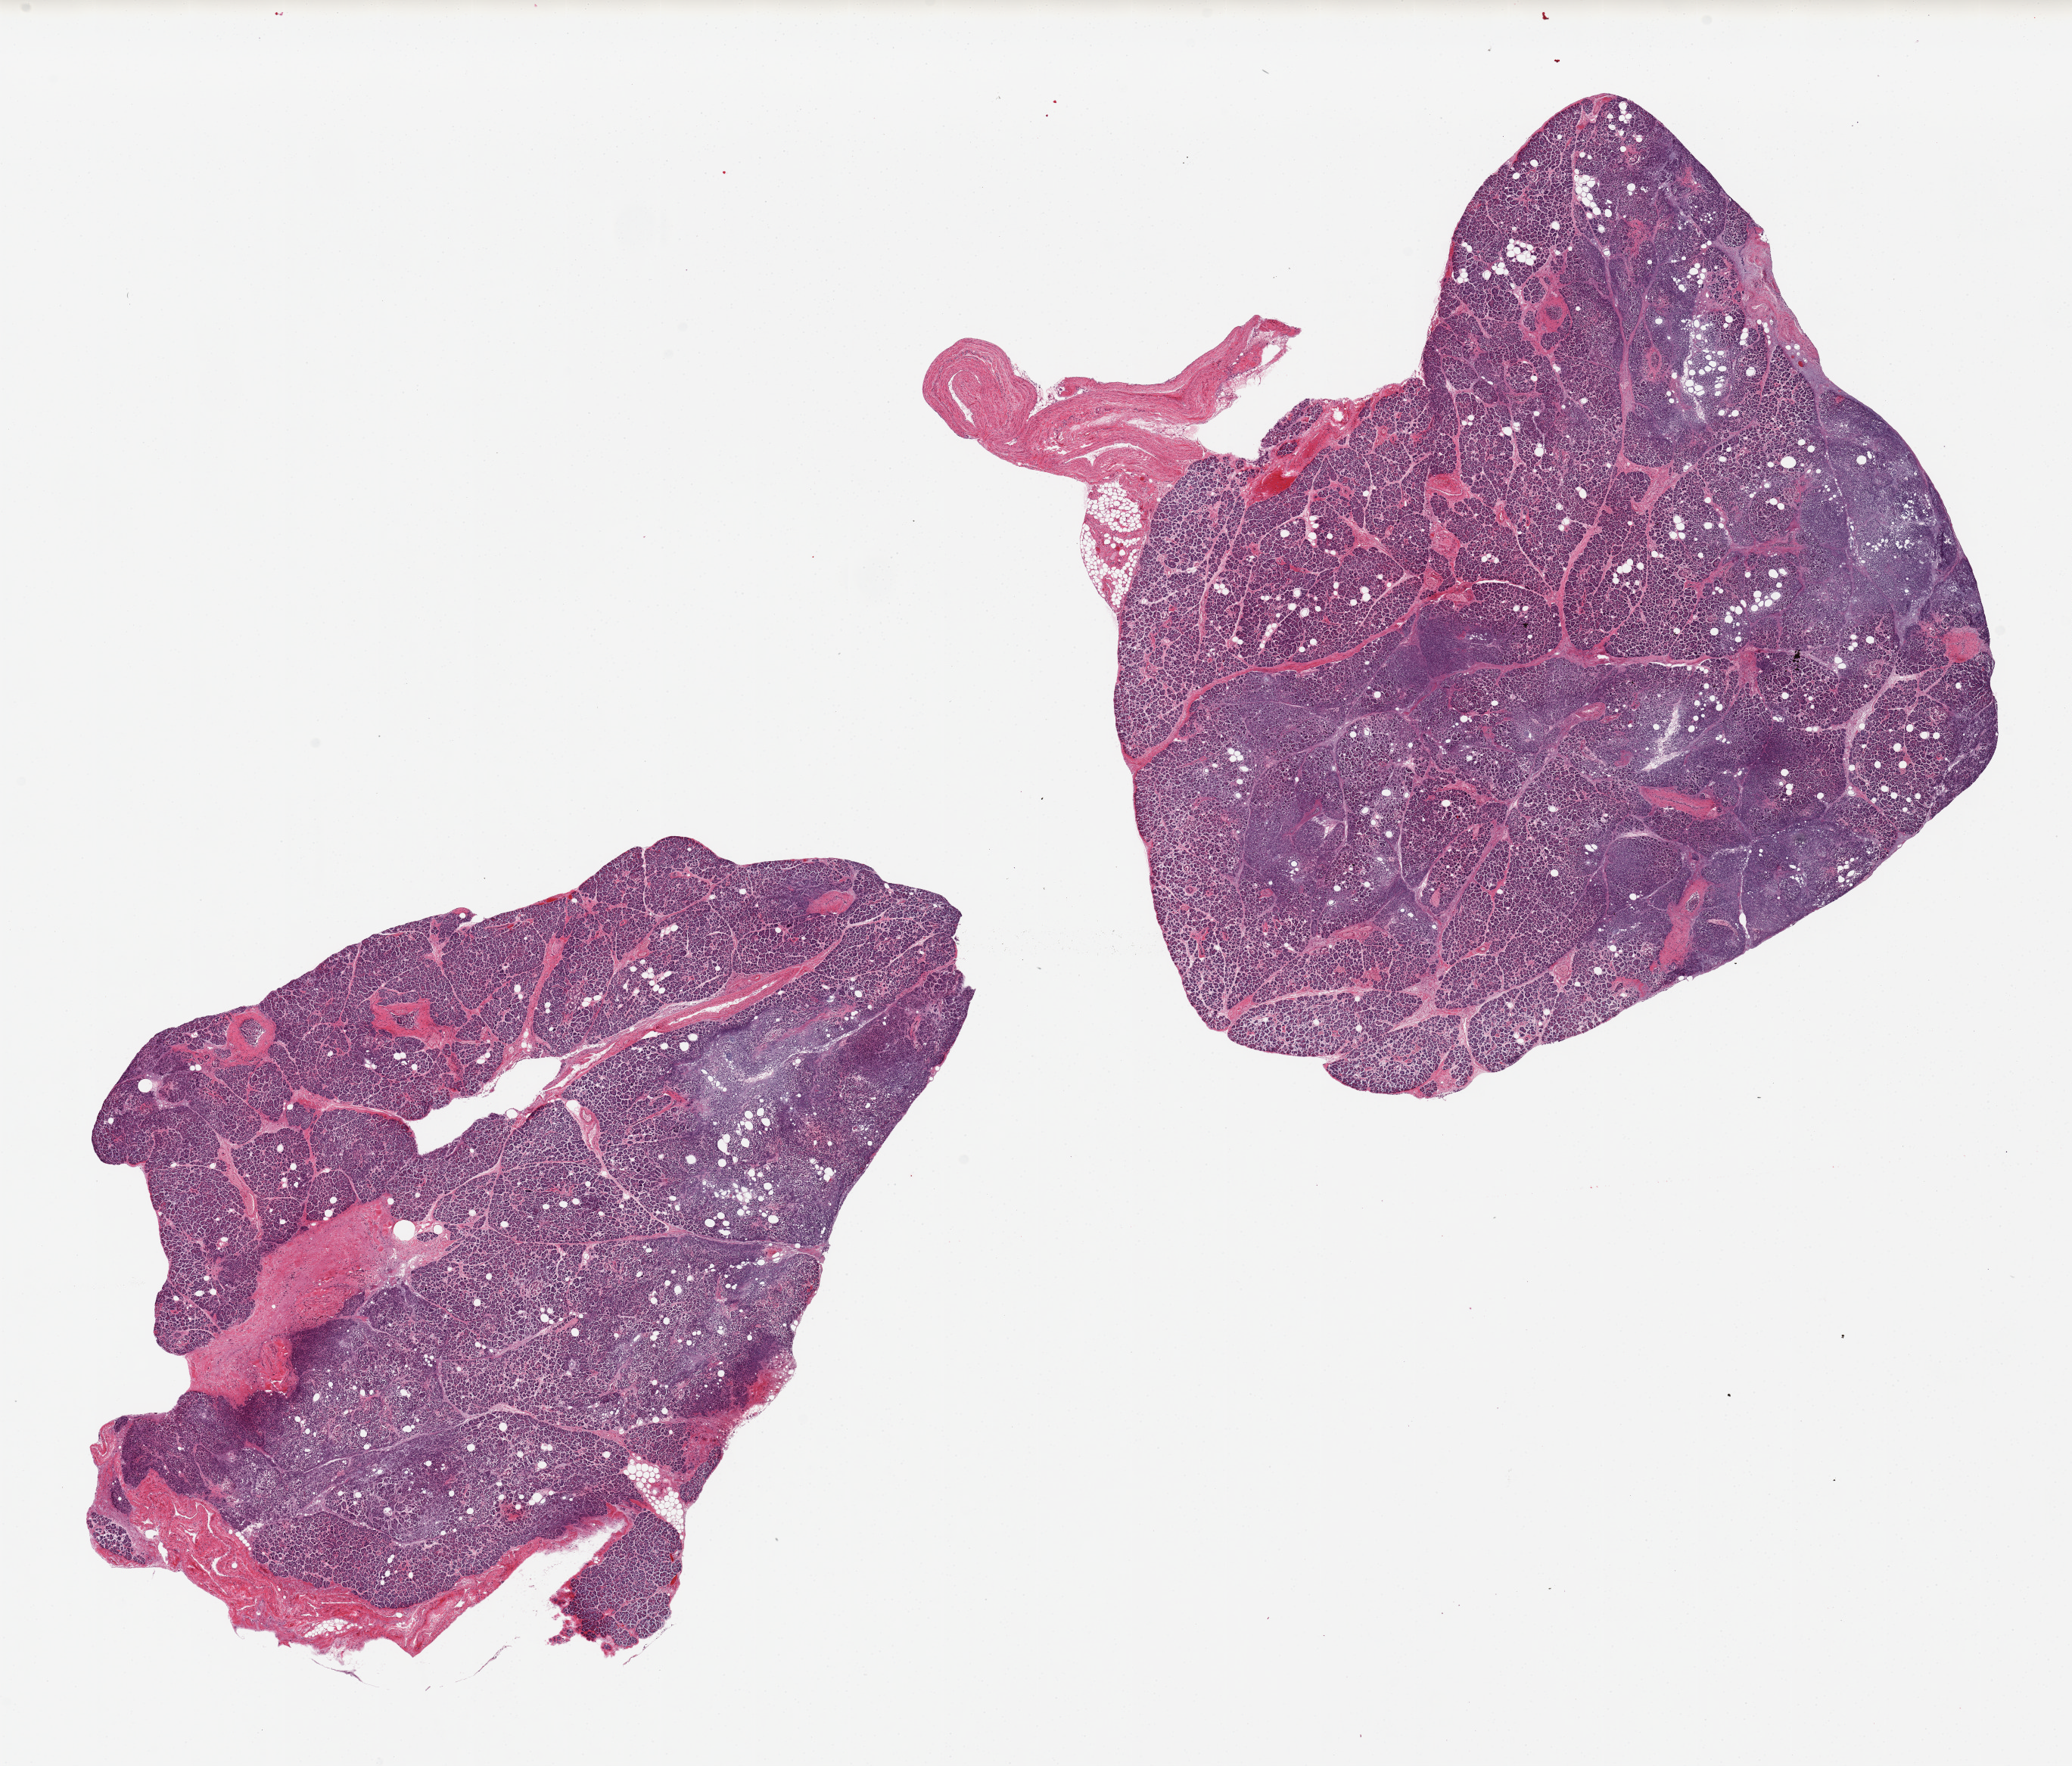
Whole-slide image, haematoxylin and eosin stain — shown as a low-resolution overview of the whole scanned area (about 21.7 x 18.5 mm, slide scanned at 20x); PAXgene-fixed, paraffin-embedded tissue; sampled site (target tissue): pancreas; donor tissue sample. Donor sex: female.
* review note (as recorded): 2 pieces, moderate/severe saponification/autolysis, Islets not well visualized